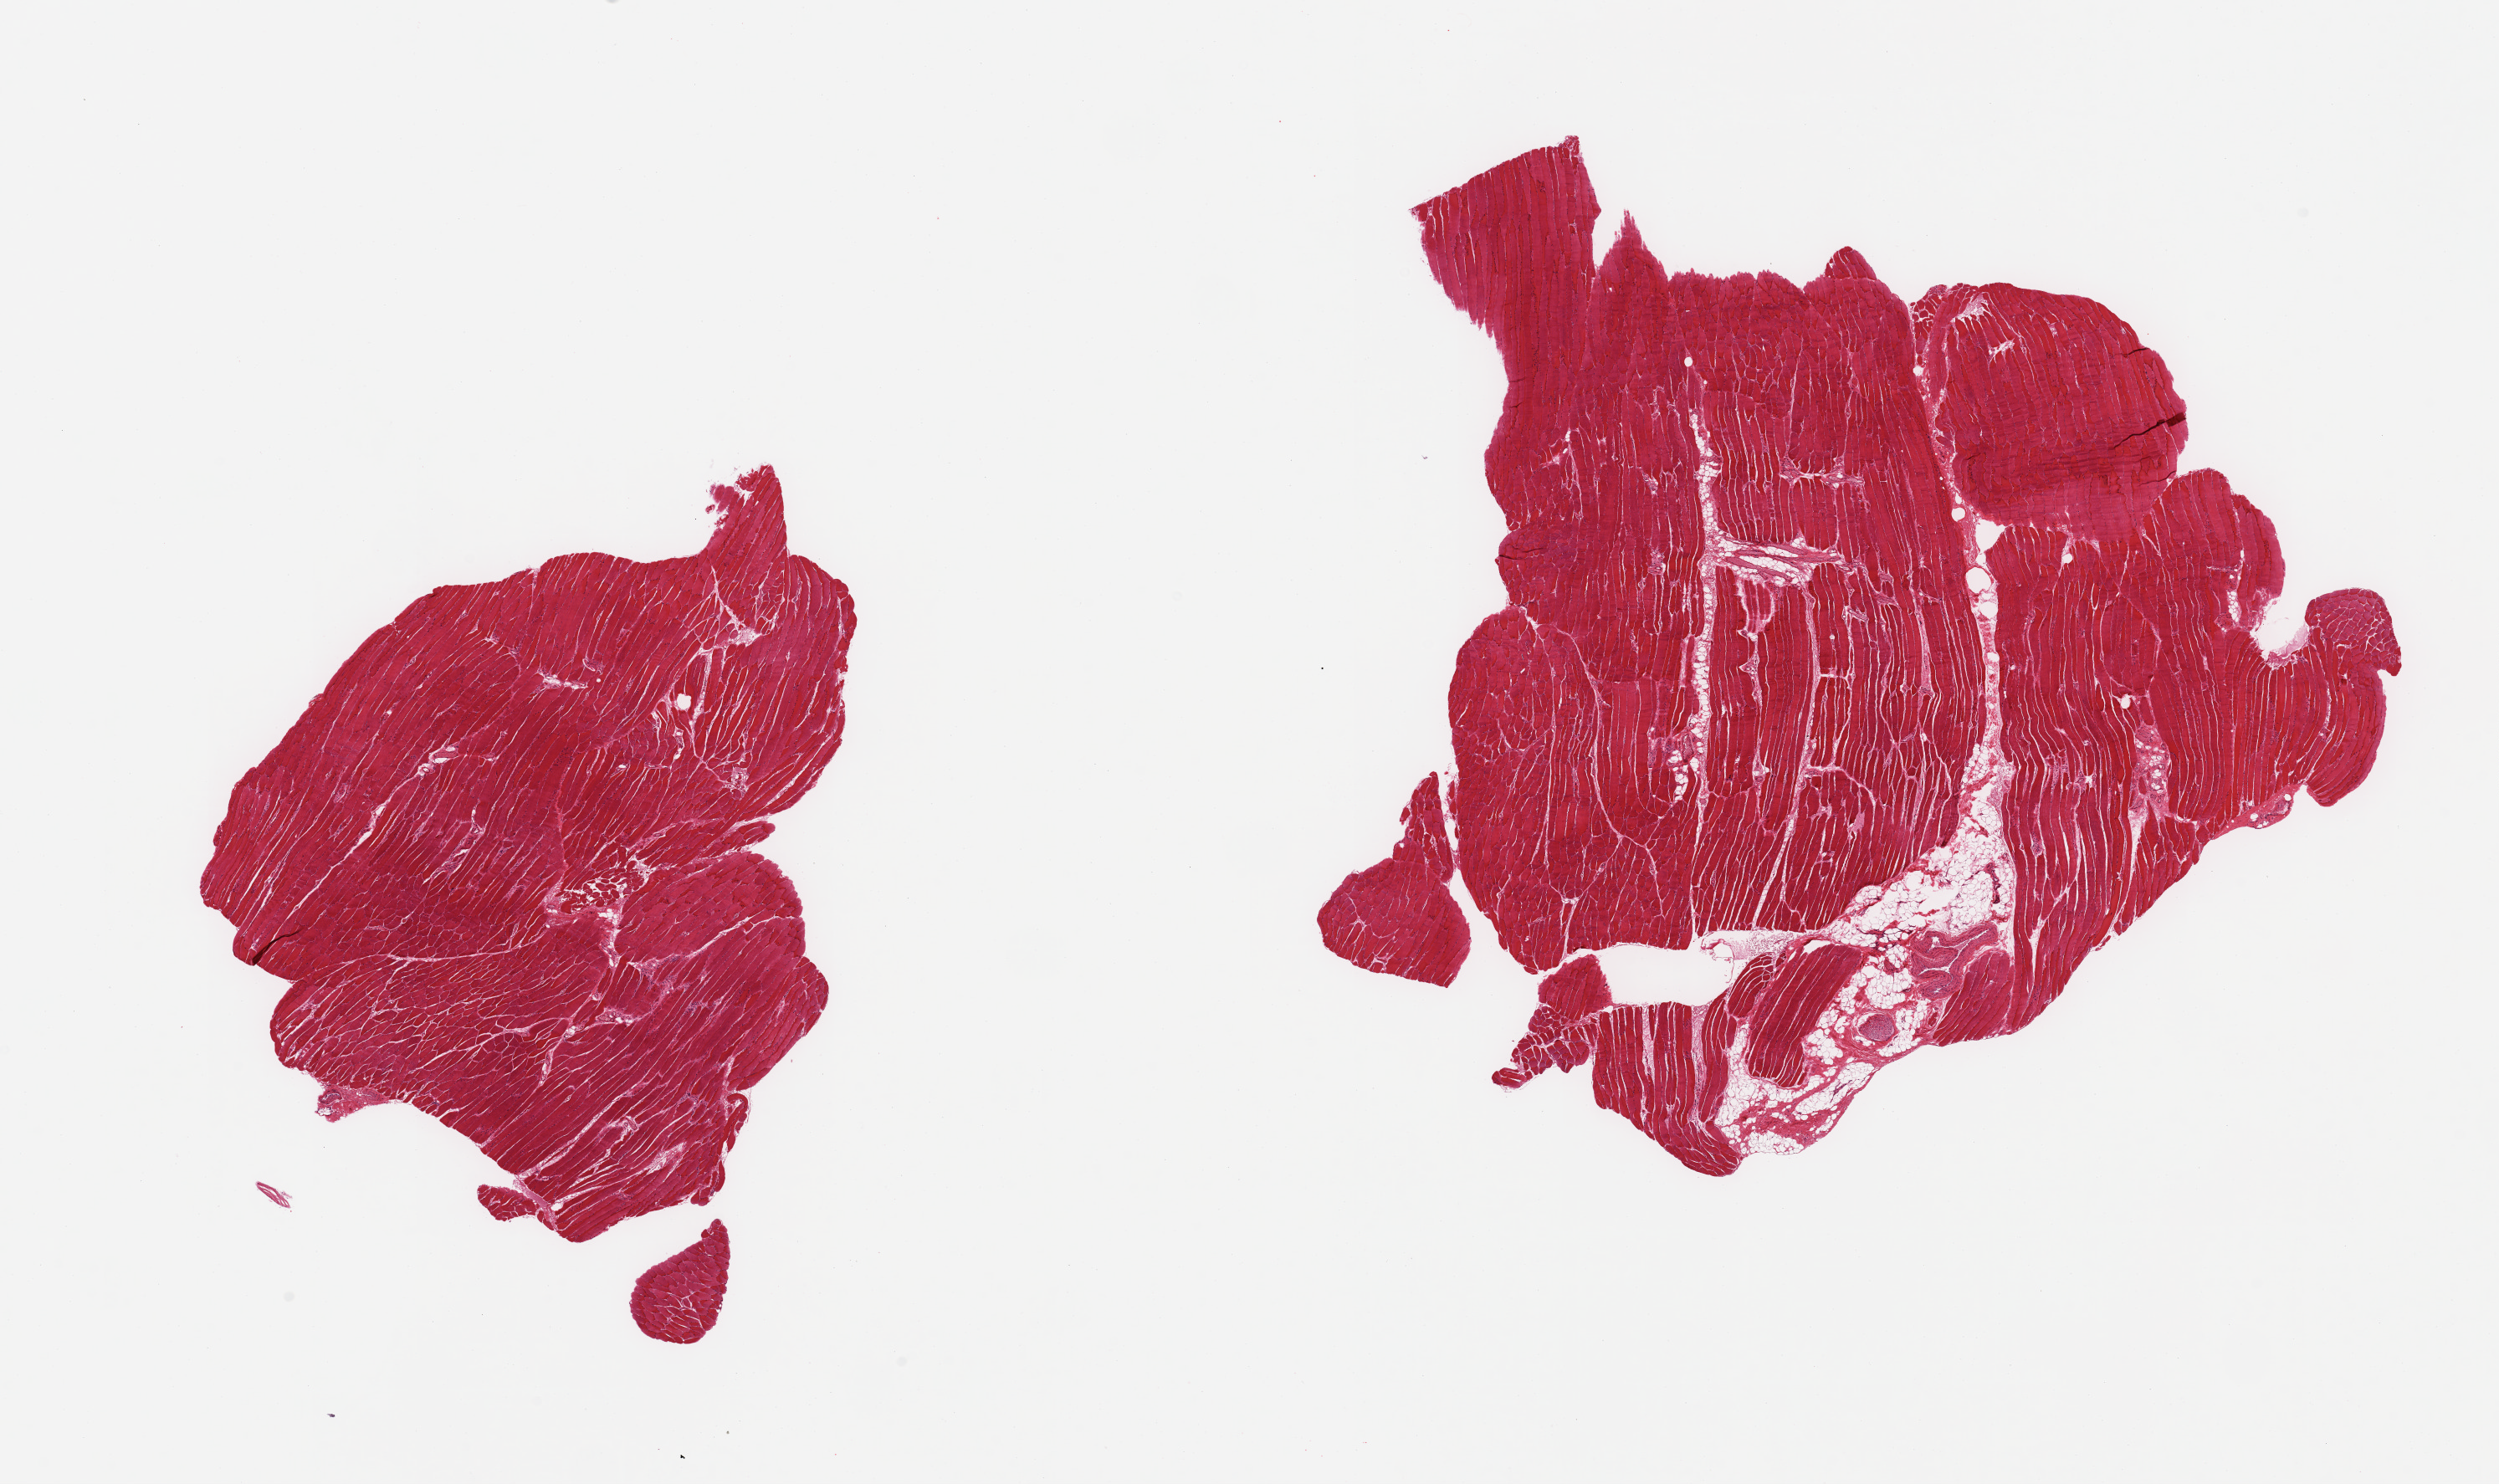
Whole-slide image, H&E stain — a low-resolution overview of the entire scanned area, about 23.6 x 14.0 mm. PAXgene-fixed paraffin-embedded (PFPE) section. Sampled site (target tissue): skeletal muscle. Tissue donor sample. Donor sex: female.
Pathologist's review note for this sample: 2 pieces; 1 piece includes up to 10% fat/nerve/vessels.